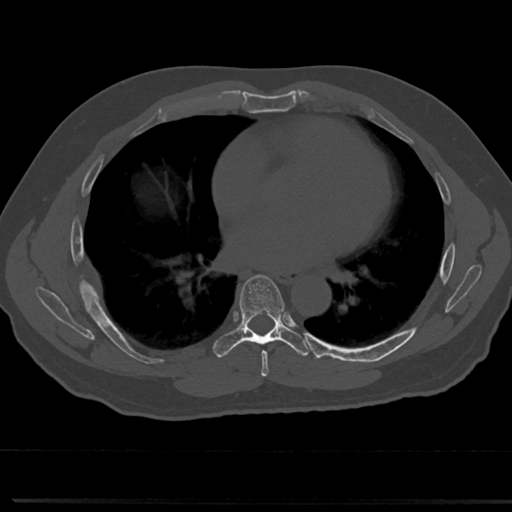
CT including the spine, one axial slice; slice 414 of 817 in the series (ordered by position); reconstruction kernel Br40s/3; 120 kVp; bone window (W 1800 / L 400 HU); 0.5 mm slice thickness; 512 × 512 image matrix. Patient: male, 61 years. Case-level facts recorded for this patient, not image findings: primary cancer: prostate.
Structures marked on this image (semi-automatic segmentation, software-assisted and operator-edited):
- T6 vertebra: bounding box [x1, y1, x2, y2] px = [243, 281, 283, 363]
- T7 vertebra: [223, 275, 286, 349]